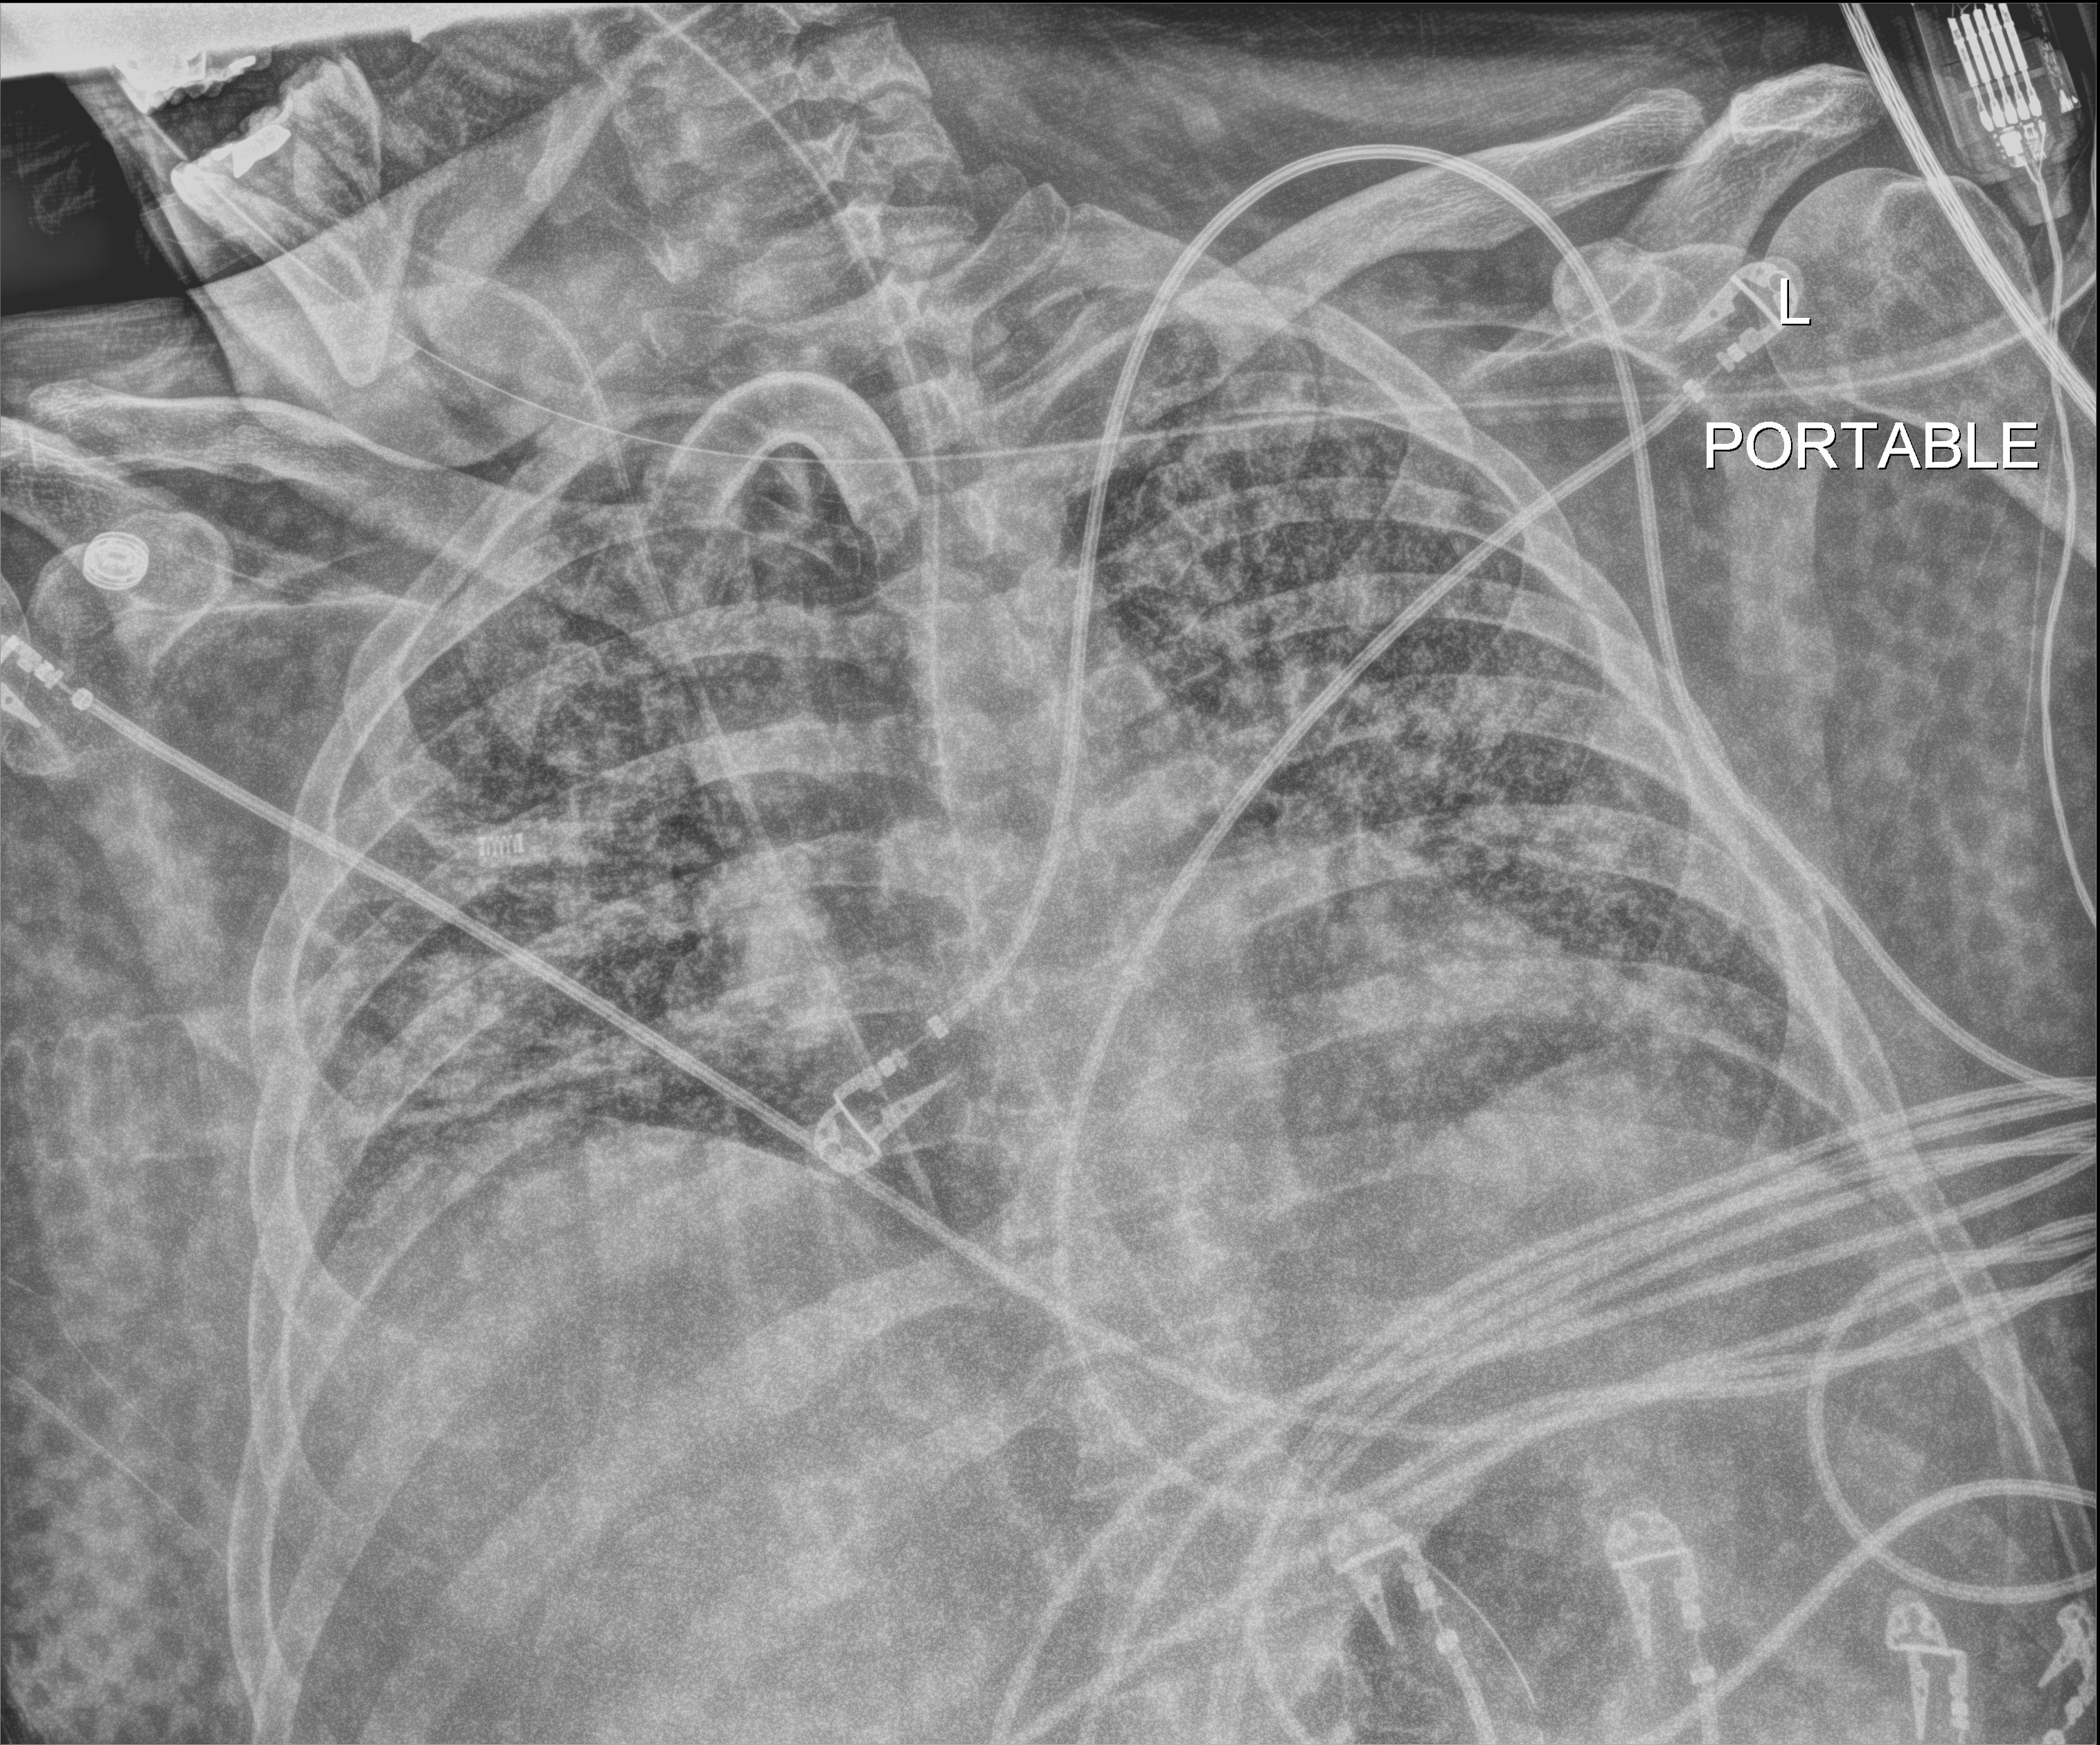
Portable chest radiograph; anteroposterior (AP) projection. Patient hospitalised with COVID-19; male, aged 18–59 years.
From the hospital-stay record, not from the radiograph (when in the stay this image was taken is not recorded):
- admitted to intensive care during this hospital stay: yes